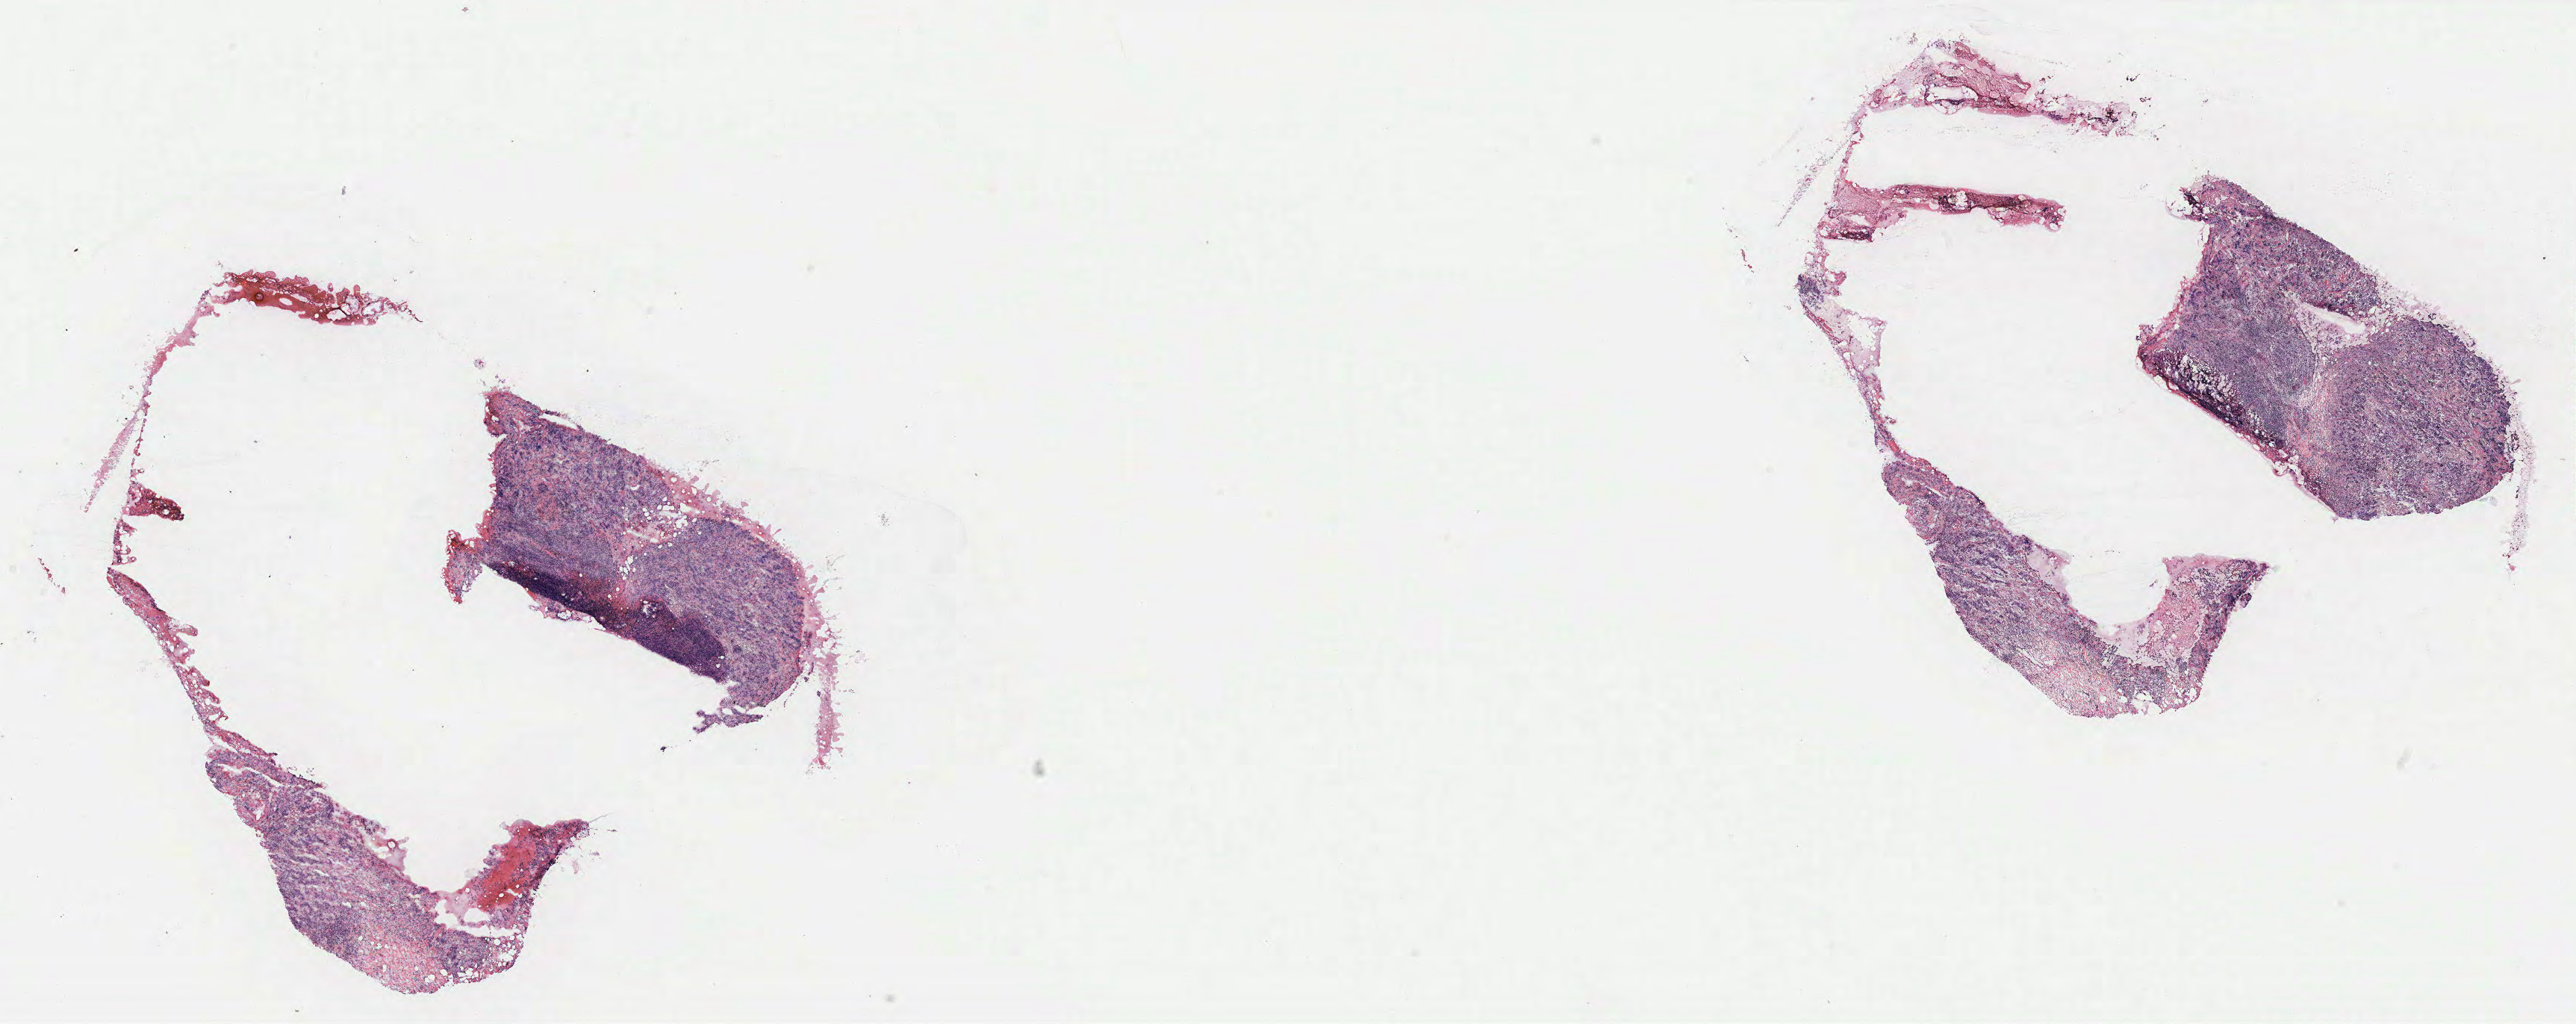
H&E-stained whole-slide image — a low-resolution overview of the entire scanned area, about 27.6 x 11.0 mm; breast, tissue type not recorded. Female, 44 y/o.
- patient diagnosis: Infiltrating duct carcinoma, NOS